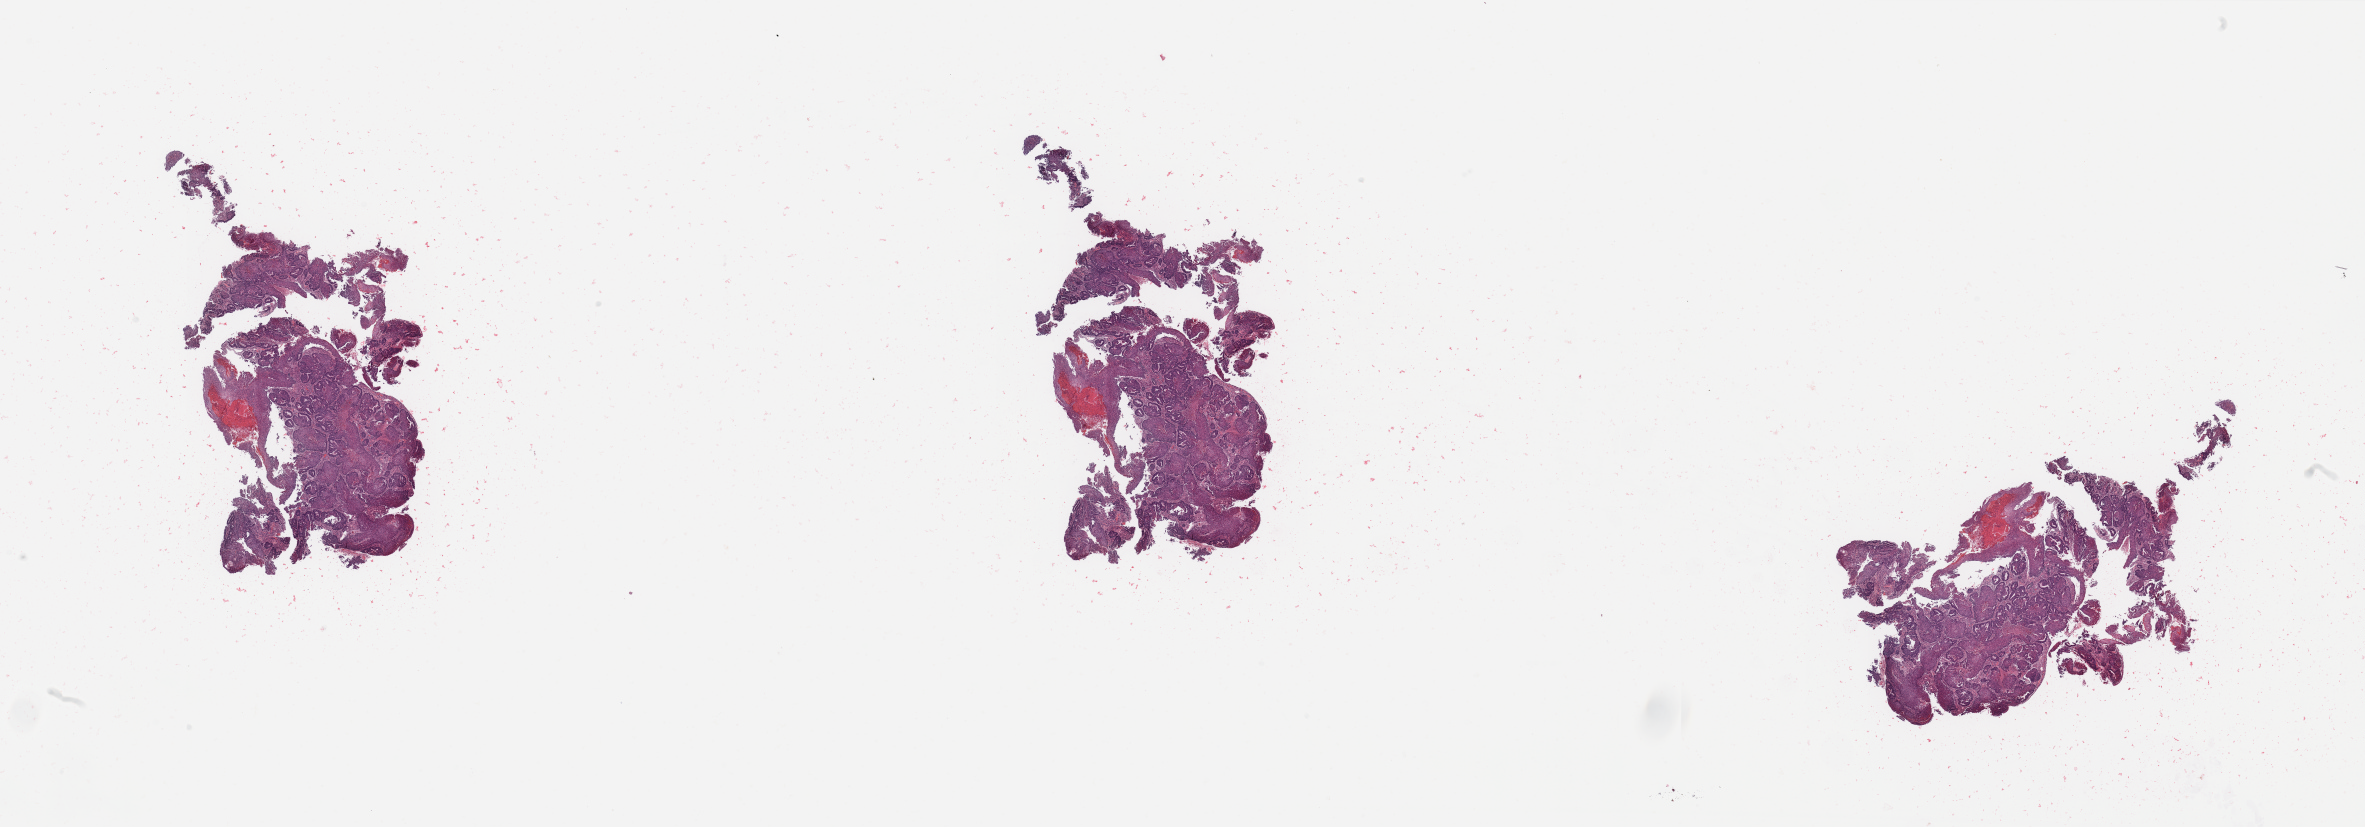
Whole-slide histology image, H&E, whole scanned area (about 37.4 x 13.1 mm) shown as a low-resolution overview. Tumour tissue sample, uterus. Female, 62 y/o. Histologic grade: G2 (moderately differentiated).
Histologic diagnosis: Endometrioid adenocarcinoma, NOS.